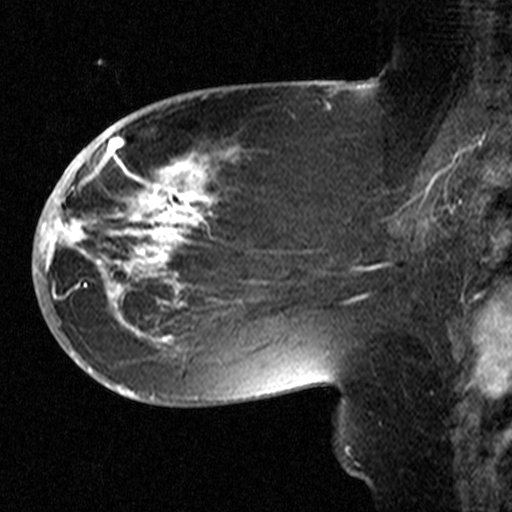
Breast MRI (dynamic contrast-enhanced), one sagittal slice. Dynamic contrast-enhanced study with each time point stored as its own series, time point 2 of 3 at this slice position (early post-contrast, ordered by acquisition time). 1.5 T. TE 4.5 ms, TR 11 ms. 3.27 mm slice thickness. 512 × 512 image matrix, field of view 200 × 200 mm. Patient: female, 53 years. From the clinical record (not read from this slice): setting: breast cancer imaged before/during neoadjuvant chemotherapy; receptor status: HR-positive, HER2-negative.
Structures marked on this image (semi-automatic segmentation, software-assisted and operator-edited):
- analysis volume of interest (the breast-tissue region the enhancement analysis was run in; not a lesion): bounding box [x1, y1, x2, y2] px = [58, 154, 311, 367]
- tumour enhancement mask (voxels above the 90 % enhancement threshold inside the analysis volume of interest): [58, 154, 214, 345]